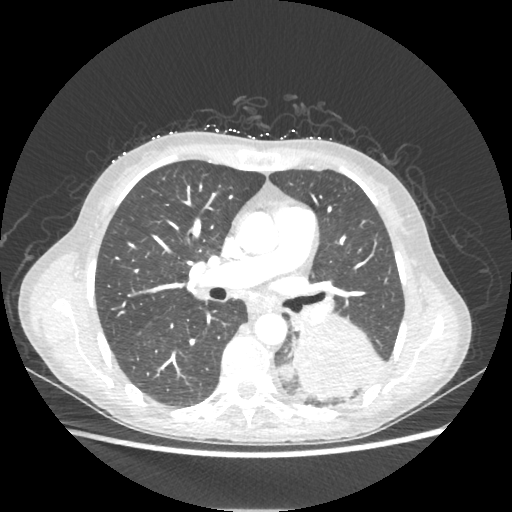
Chest CT, one axial slice. Slice 123 of 221 in the series (ordered by position). Reconstruction kernel STANDARD. 80 kVp. Lung window (W 1500 / L -600 HU). 512 × 512 image matrix, field of view 360 × 360 mm. Female patient, age 53 years. From the clinical record (not read from this slice): clinical TNM (as recorded): T3 N0 M0.
Structures marked on this image (bounding box drawn by a radiologist):
- lung tumour (recorded histology: adenocarcinoma): bounding box <291,318,385,400> (left, top, right, bottom; pixels)